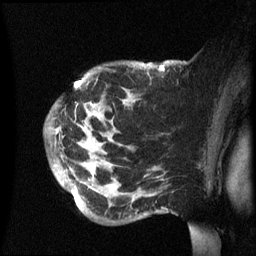
Breast MRI (dynamic contrast-enhanced), one sagittal slice. Position 44 of 60 along the scan axis. Dynamic contrast-enhanced series, image 2 of 3 at this slice position (ordered by acquisition). 1.5 T. TE 4.2 ms, TR 8.4 ms. 2.4 mm slice thickness. 256 × 256 image matrix. Female patient, age 49 years.
Structures marked on this image (semi-automatically segmented with operator editing):
- analysis volume of interest (the breast-tissue region the enhancement analysis was run in; not a lesion): box from (x=44, y=60) to (x=174, y=223) px
- tumour enhancement mask (voxels above the 70 % enhancement threshold inside the analysis volume of interest): (x=72, y=65)–(x=164, y=192)